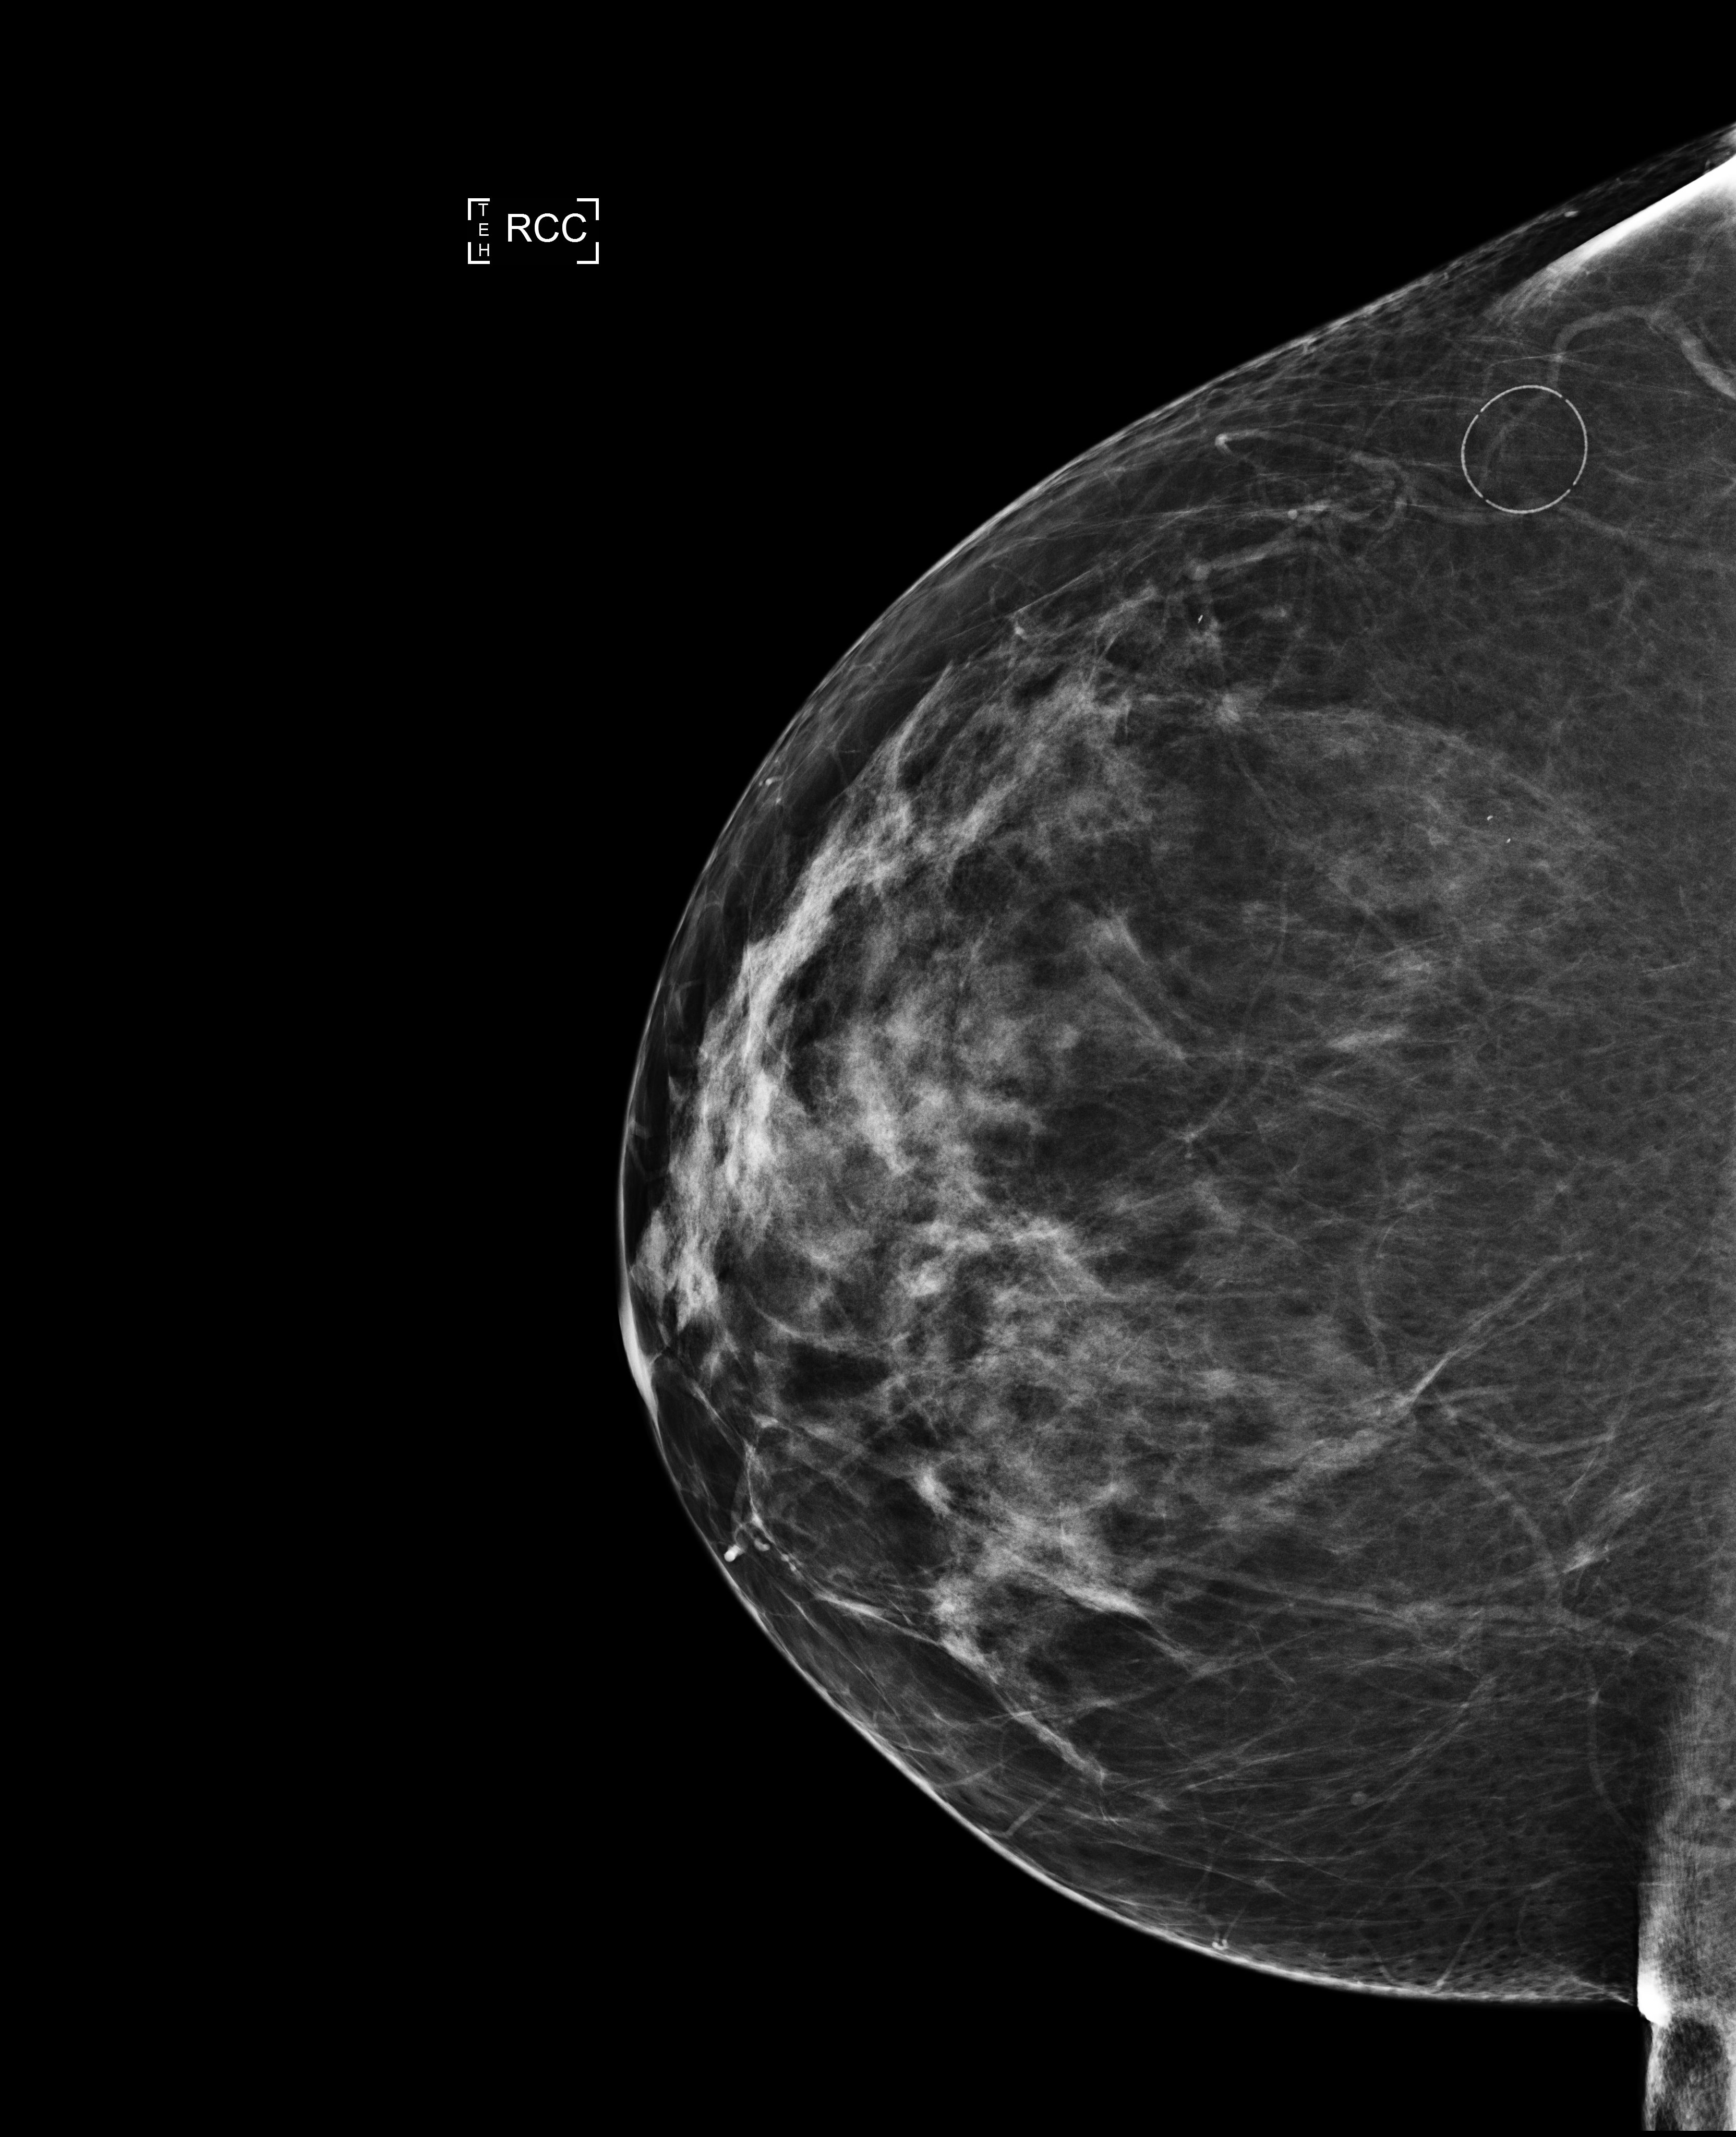
Annual screening mammography examination. Female patient, age 65 years.
Image type: full-field digital mammogram. Breast: right. Projection: cranio-caudal projection.